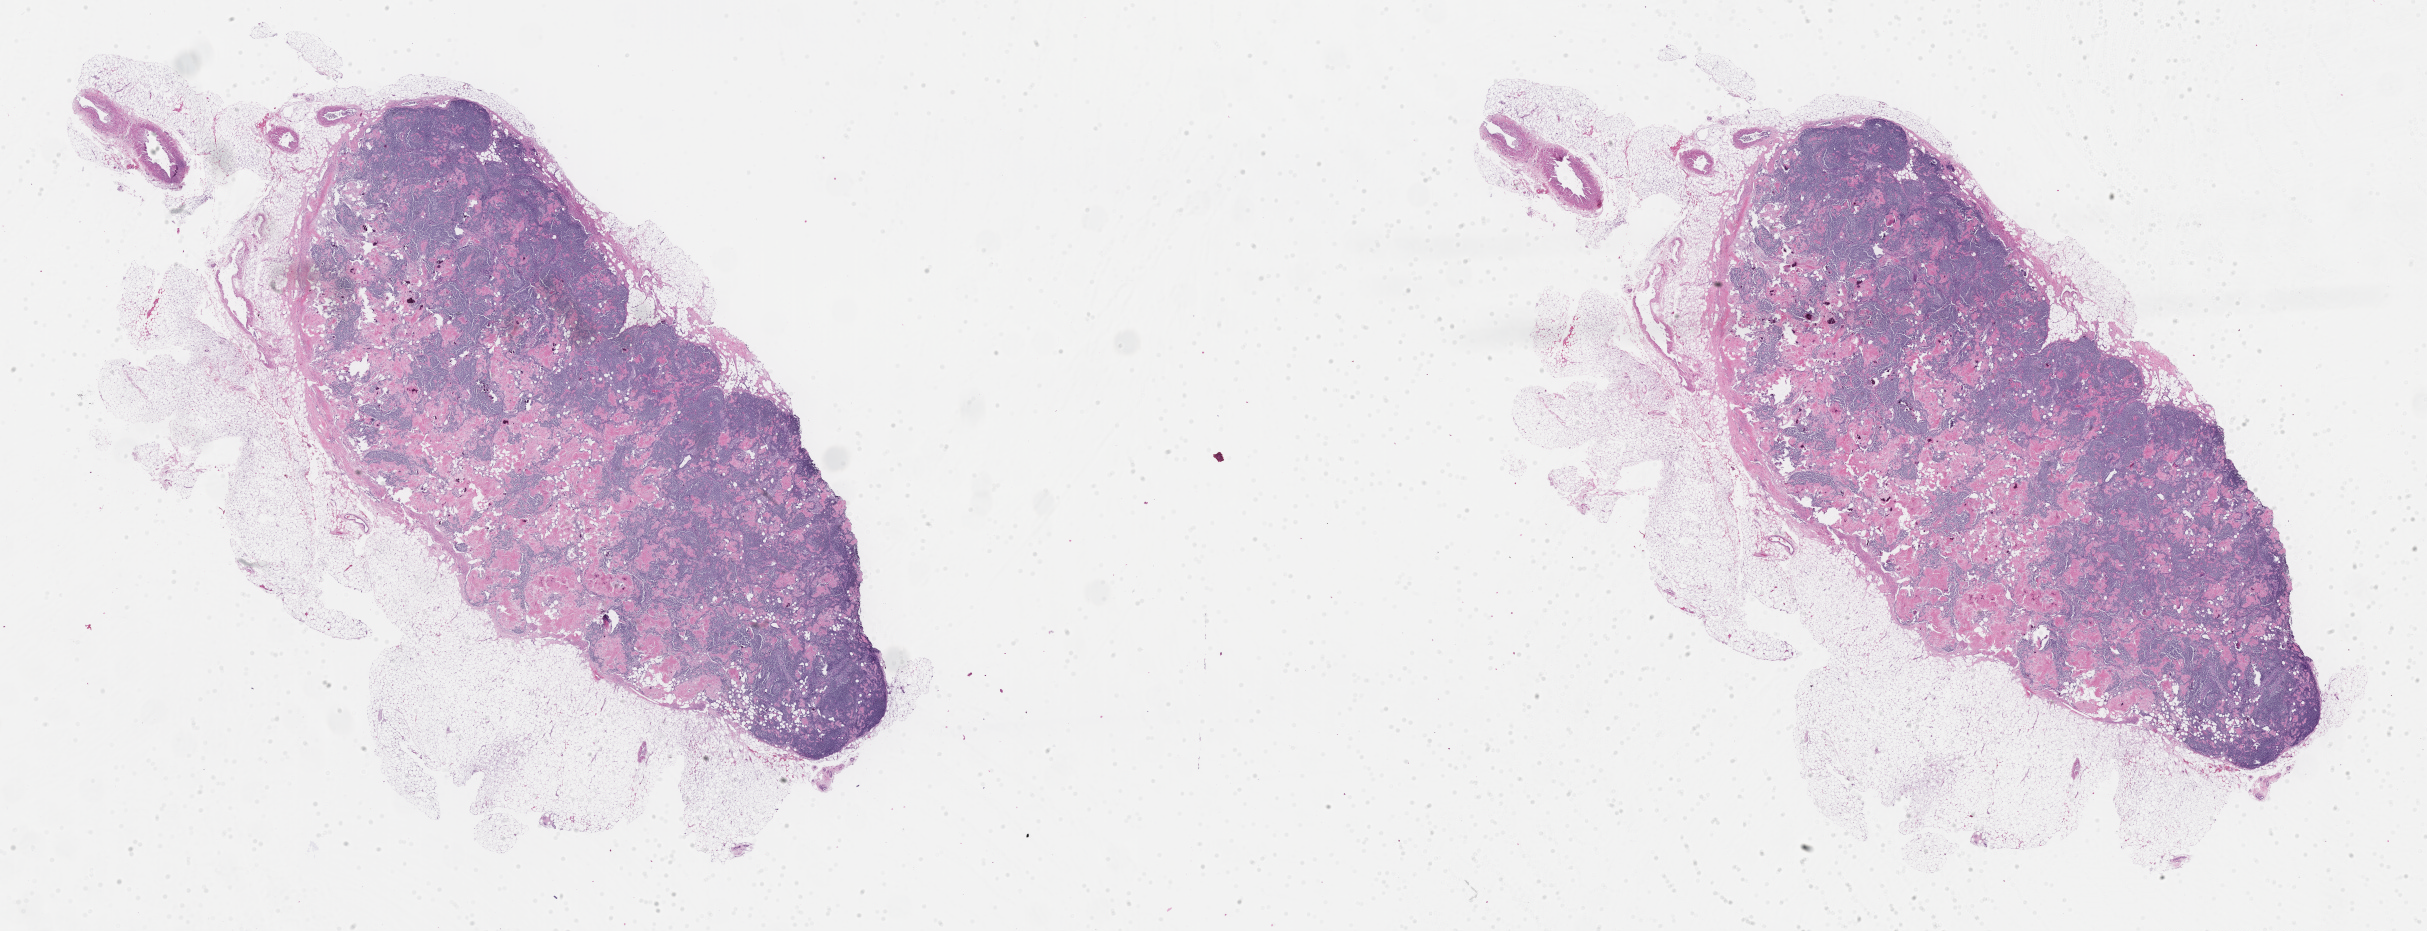
Hematoxylin and eosin (H&E) whole-slide image — whole scanned area (about 39.2 x 15.0 mm) shown as a low-resolution overview, formalin-fixed paraffin-embedded section, specimen: normal-tissue sample (non-tumor) from a patient with papillary urothelial carcinoma, site: bladder. Male patient; age at initial diagnosis 84 years. Pathologist review of this section (percent, as recorded): tumor cells 0%, tumor nuclei 0%, stromal cells 100%, necrosis 0%, normal cells 0%. Inflammatory infiltration, as recorded: lymphocyte infiltration 100%, monocyte infiltration 0%, neutrophil infiltration 0%.
This section: non-tumor tissue sample; the patient's diagnosis is given above.